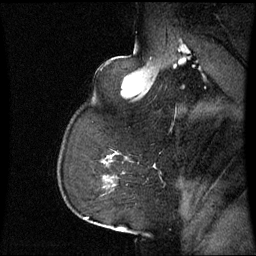
Breast MRI (dynamic contrast-enhanced), one sagittal slice; dynamic contrast-enhanced series, image 2 of 3 at this slice position (ordered by acquisition); 1.5 T; TE 4.2 ms, TR 8.9 ms; 2.4 mm slice thickness; 256 × 256 image matrix. Female patient, age 59 years. Case-level facts recorded for this patient, not image findings: setting: breast cancer imaged before/during neoadjuvant chemotherapy; receptor status: triple-negative.
Annotated regions visible in this slice (semi-automatic segmentation, software-assisted and operator-edited):
- analysis volume of interest (the breast-tissue region the enhancement analysis was run in; not a lesion): bounding box (x1, y1, x2, y2) in pixels: (104, 152, 127, 189)
- tumour enhancement mask (voxels above the 70 % enhancement threshold inside the analysis volume of interest): (104, 158, 113, 163)